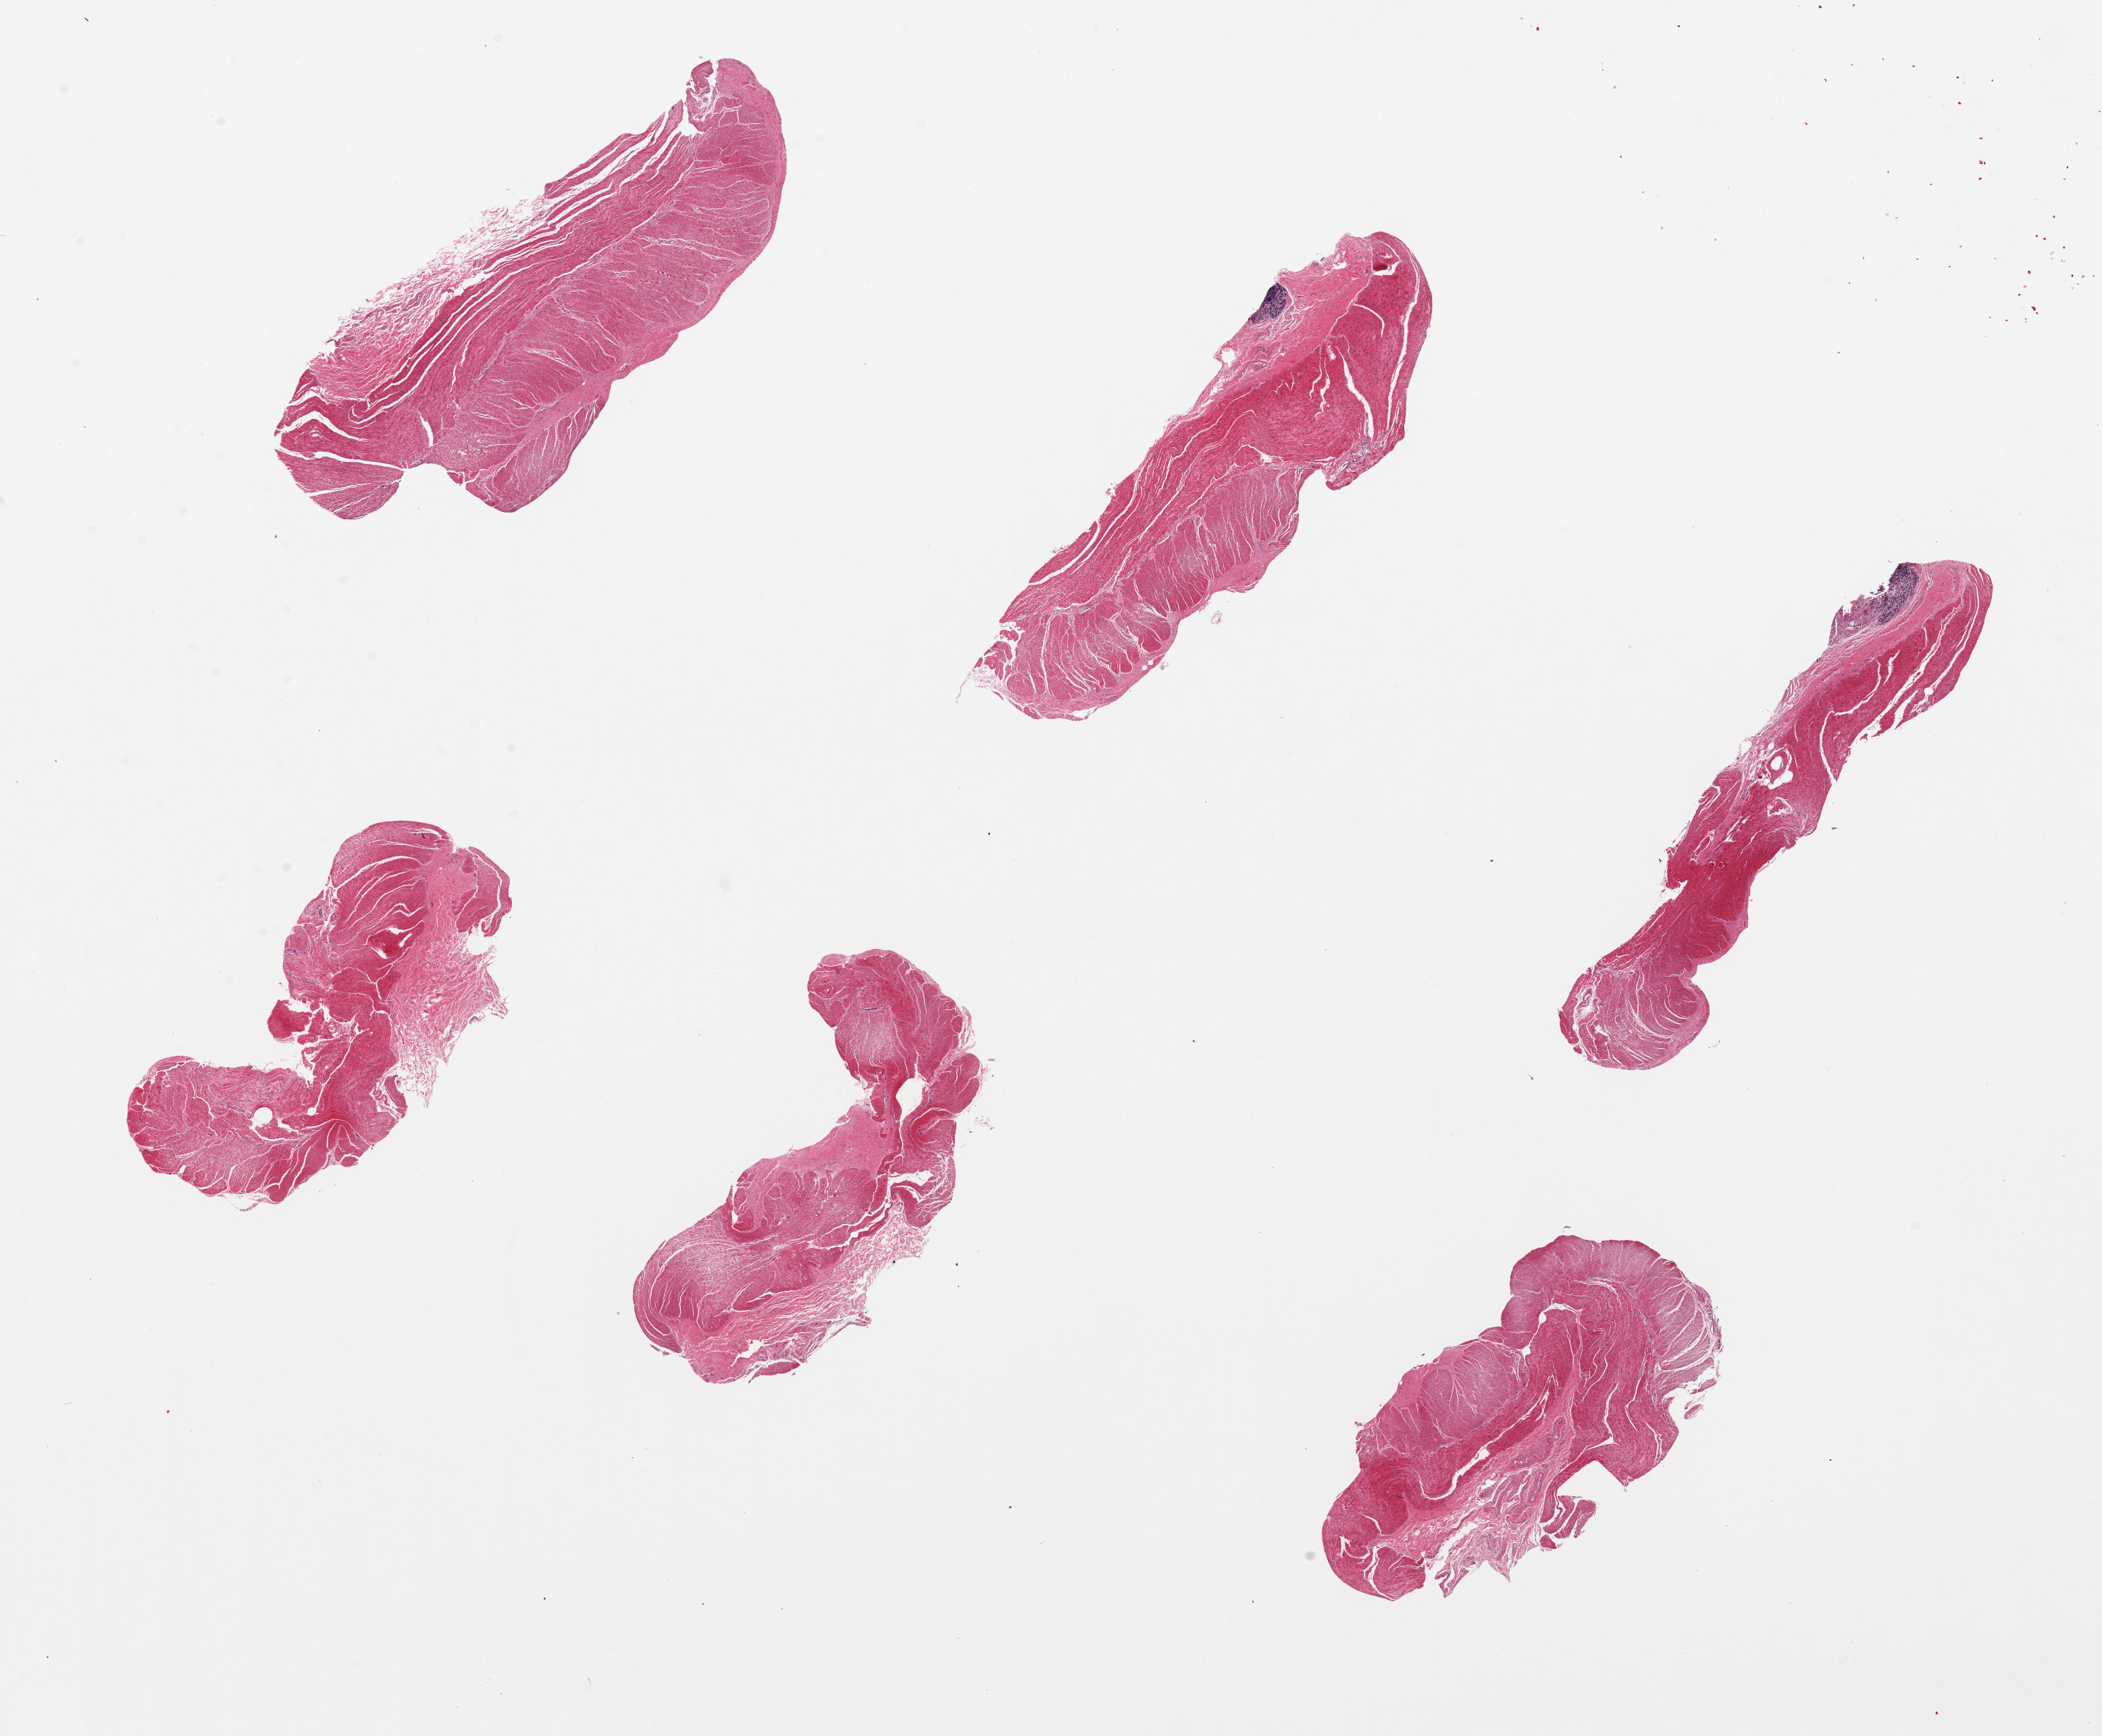
Digitized haematoxylin and eosin-stained section, brightfield, shown as a low-resolution overview of the whole scanned area (about 24.6 x 20.3 mm). PAXgene-fixed, paraffin-embedded tissue. Sampled site (target tissue): sigmoid colon. Donor tissue sample. Donor sex: male.
Reviewer comment on this tissue sample: 6 pieces; predominantly muscularis with two foci of residual autolyzed mucosa/lymphoid tissue.